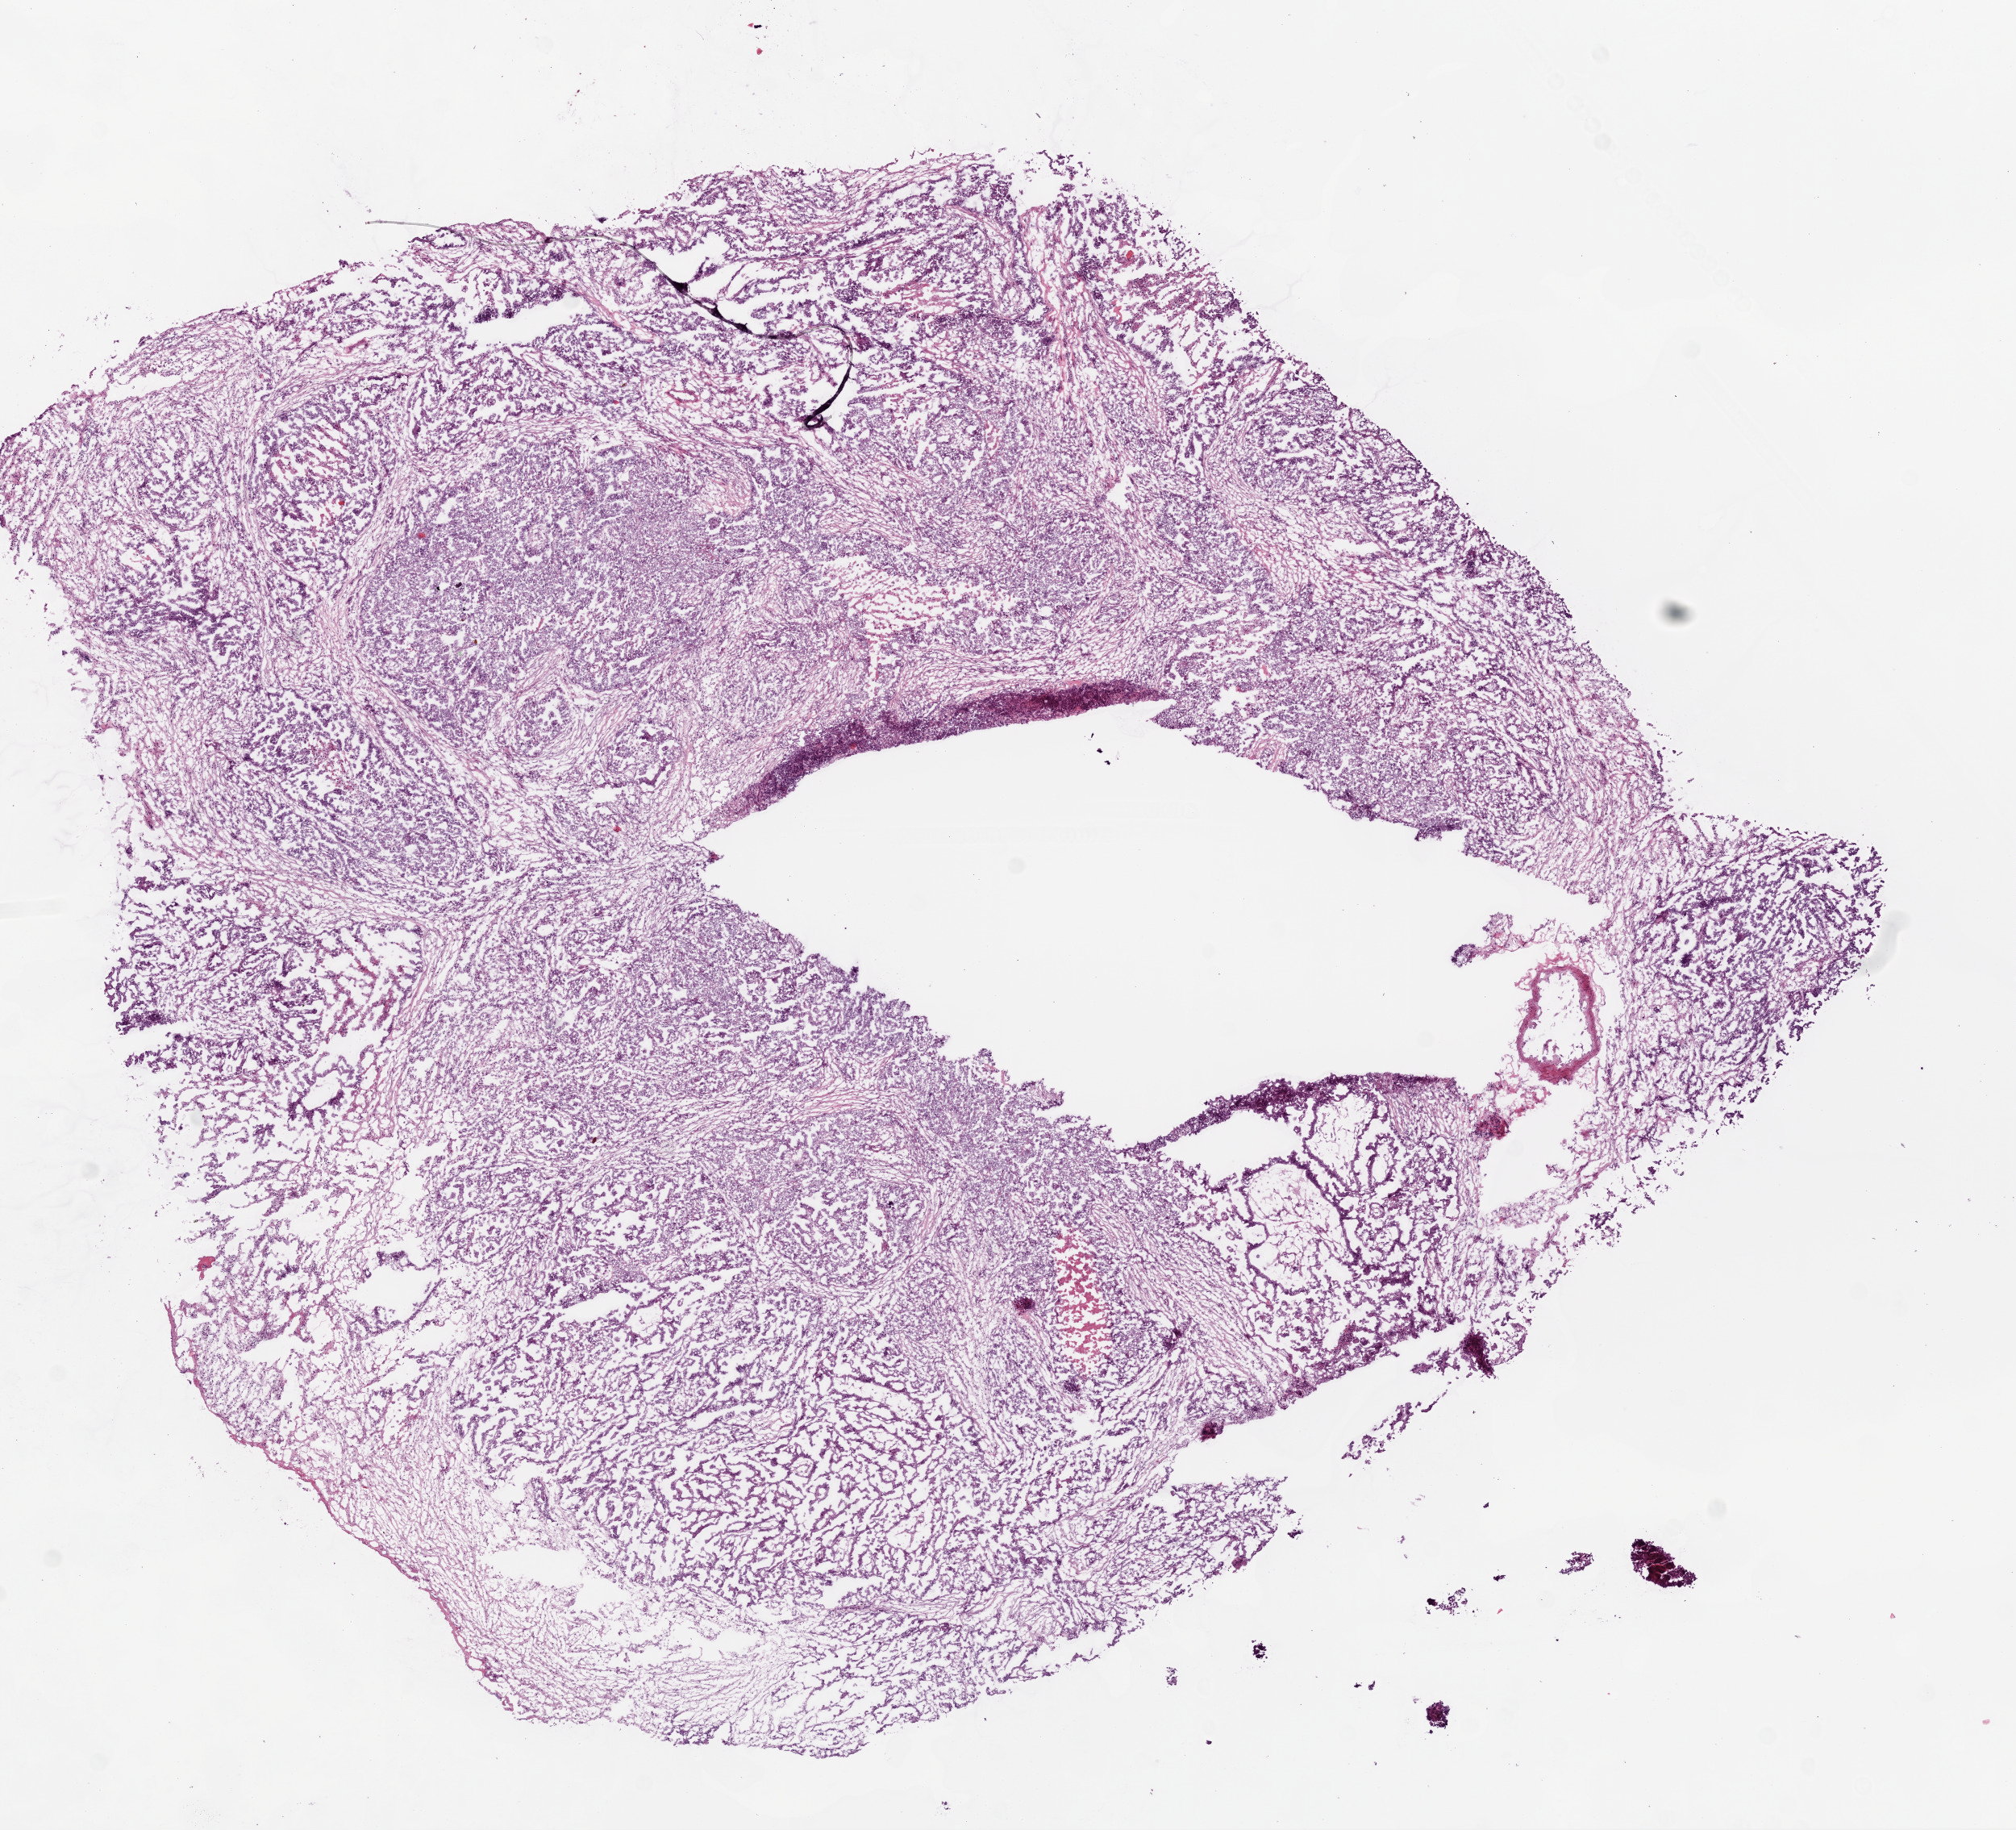
Digitized H&E tissue section (whole slide), a low-resolution overview of the entire scanned area, about 10.0 x 9.1 mm (slide scanned at 20x); frozen section from the bottom of the tissue portion; ovary, primary tumour sample. Patient: female, age at initial diagnosis 49 years. Histologic grade: G2 (moderately differentiated). Composition of this section per pathologist review: tumour cells 90%, tumour nuclei 70%, normal cells 0%, stromal cells 0%, necrosis 10%. Inflammatory infiltration, as recorded: lymphocyte infiltration 5%, monocyte infiltration 3%.
• FIGO stage: IIIC
• laterality: bilateral
• diagnosis: Serous cystadenocarcinoma, NOS